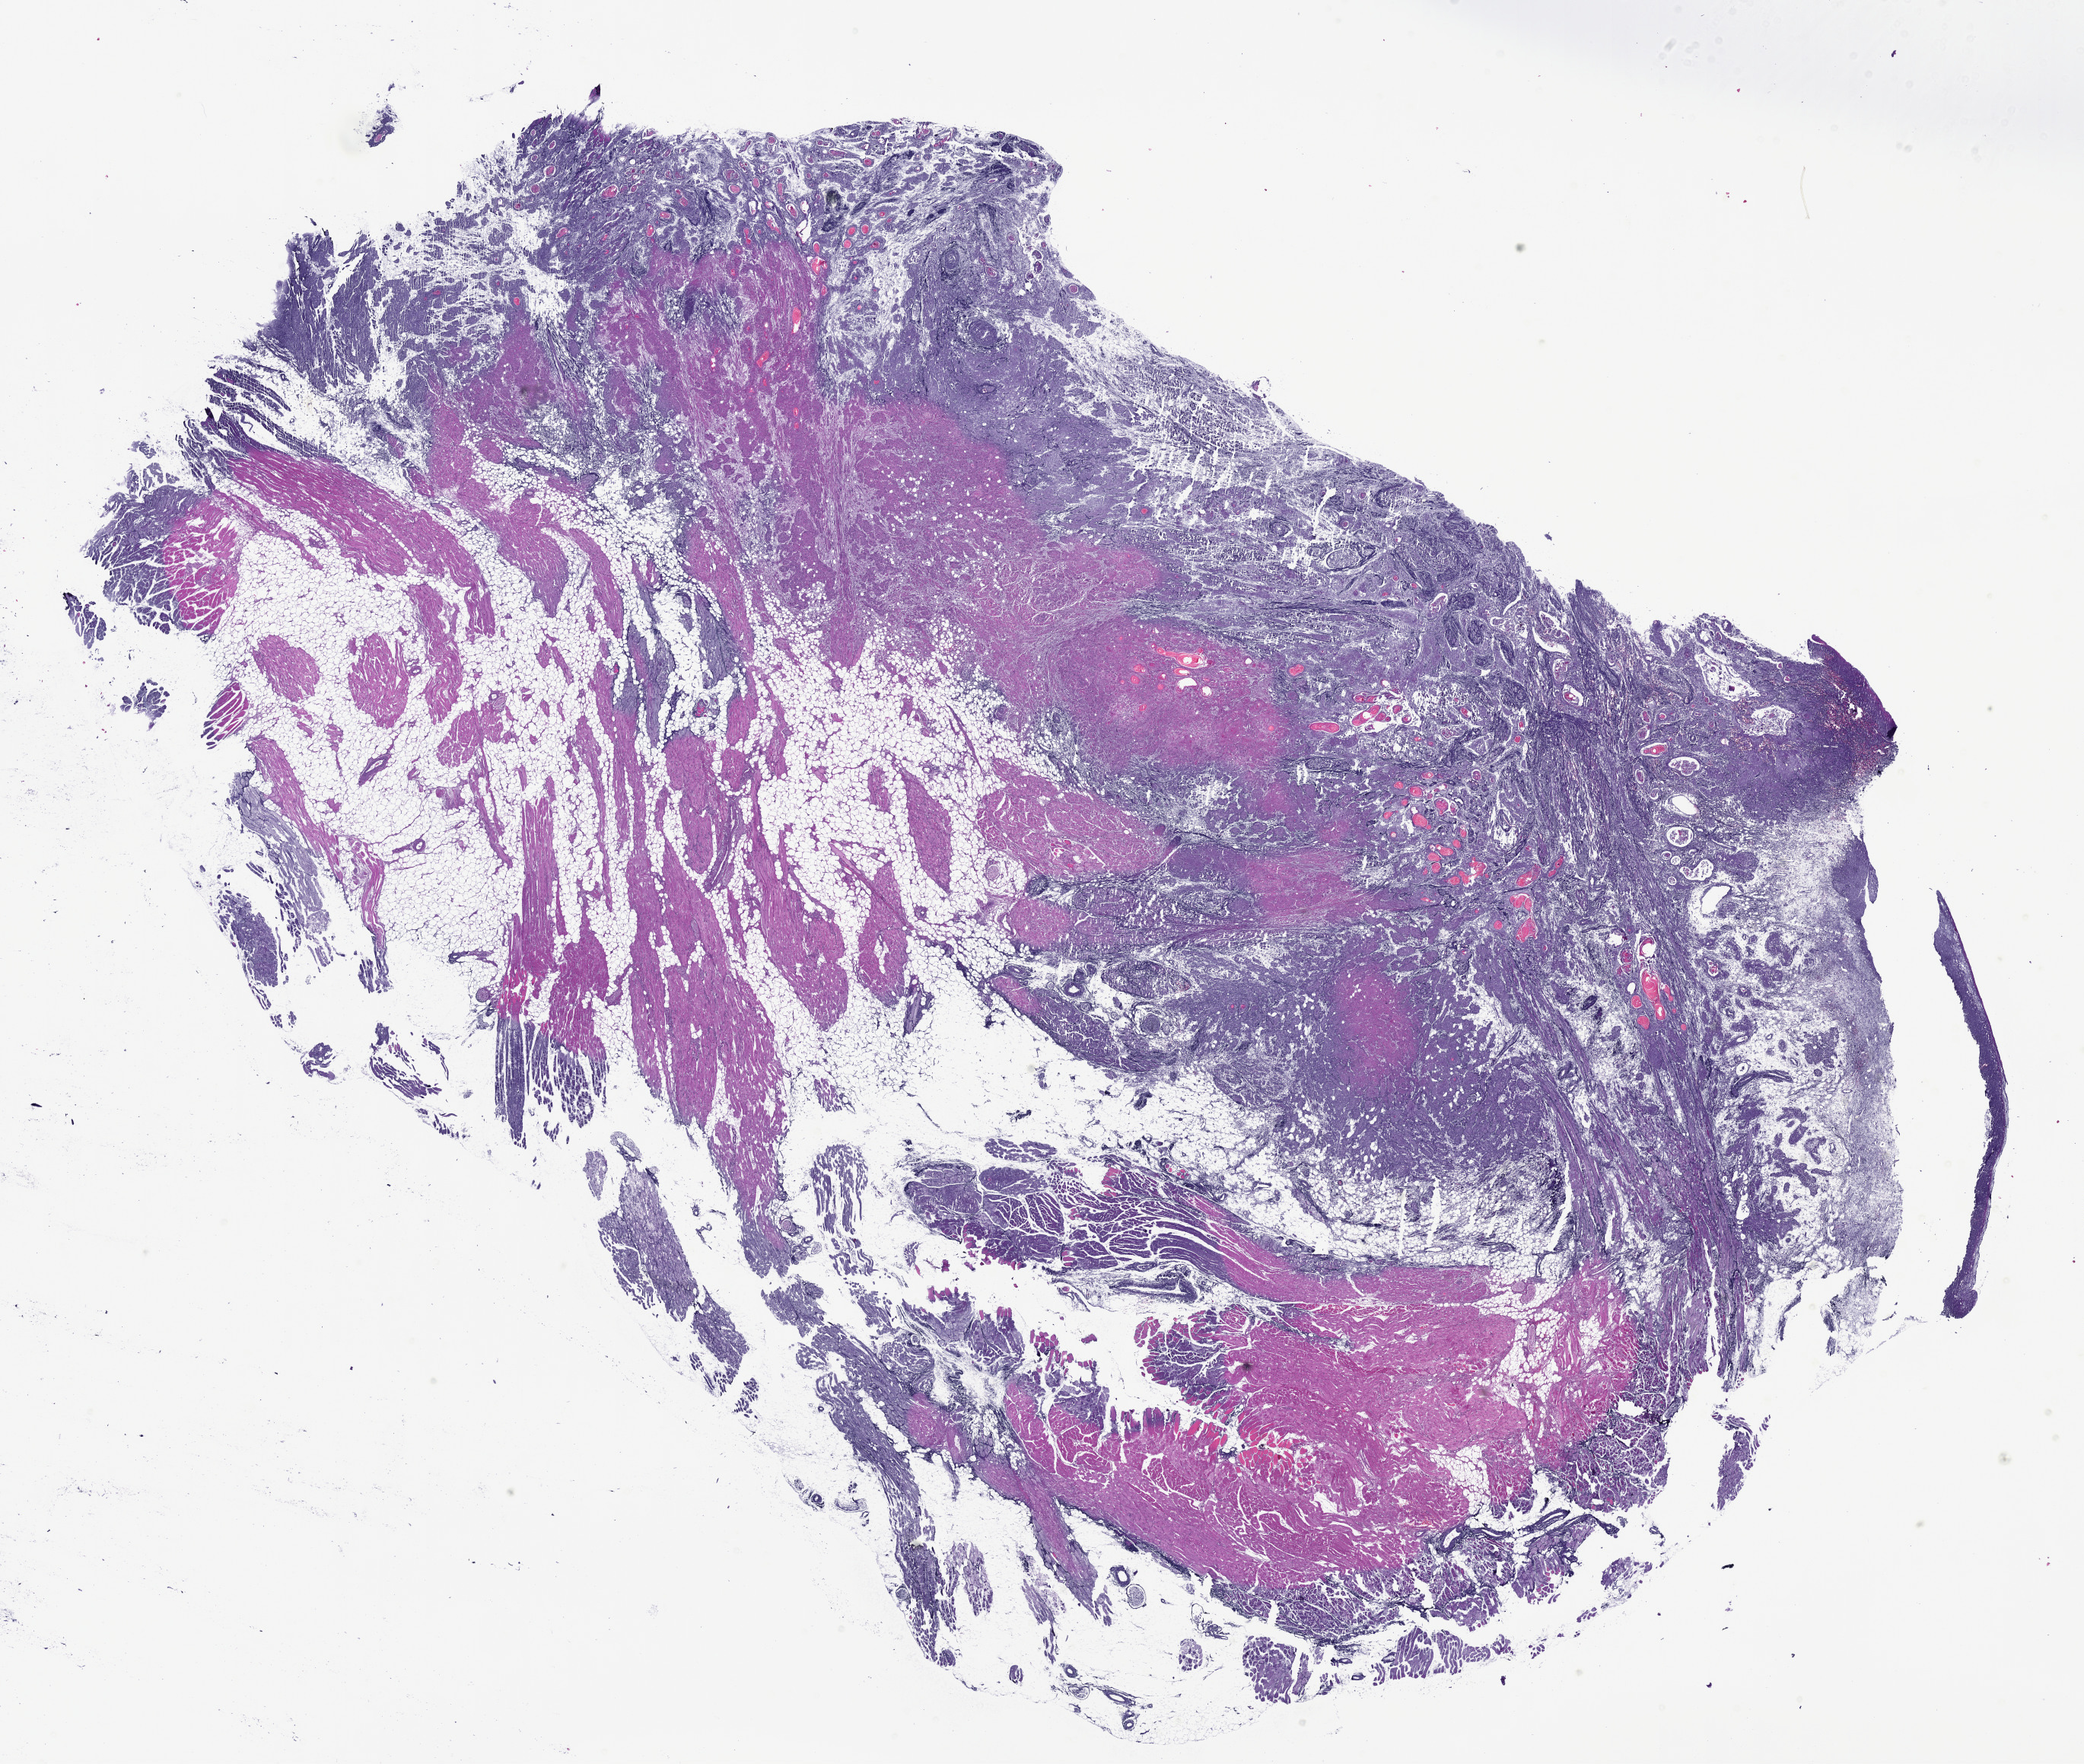
Digitized H&E tissue section (whole slide) — whole scanned area (about 22.1 x 18.7 mm, acquisition: 40x scan) shown as a low-resolution overview, formalin-fixed paraffin-embedded (FFPE) diagnostic section, head and neck, primary tumour sample. Female patient; age at initial diagnosis 61 years. Histologic grade: G2 (moderately differentiated).
Pathologic diagnosis: Squamous cell carcinoma, keratinizing, NOS. Lymph nodes positive (case pathology): 8 of 30 examined. AJCC pathologic stage: IVA (7th edition).